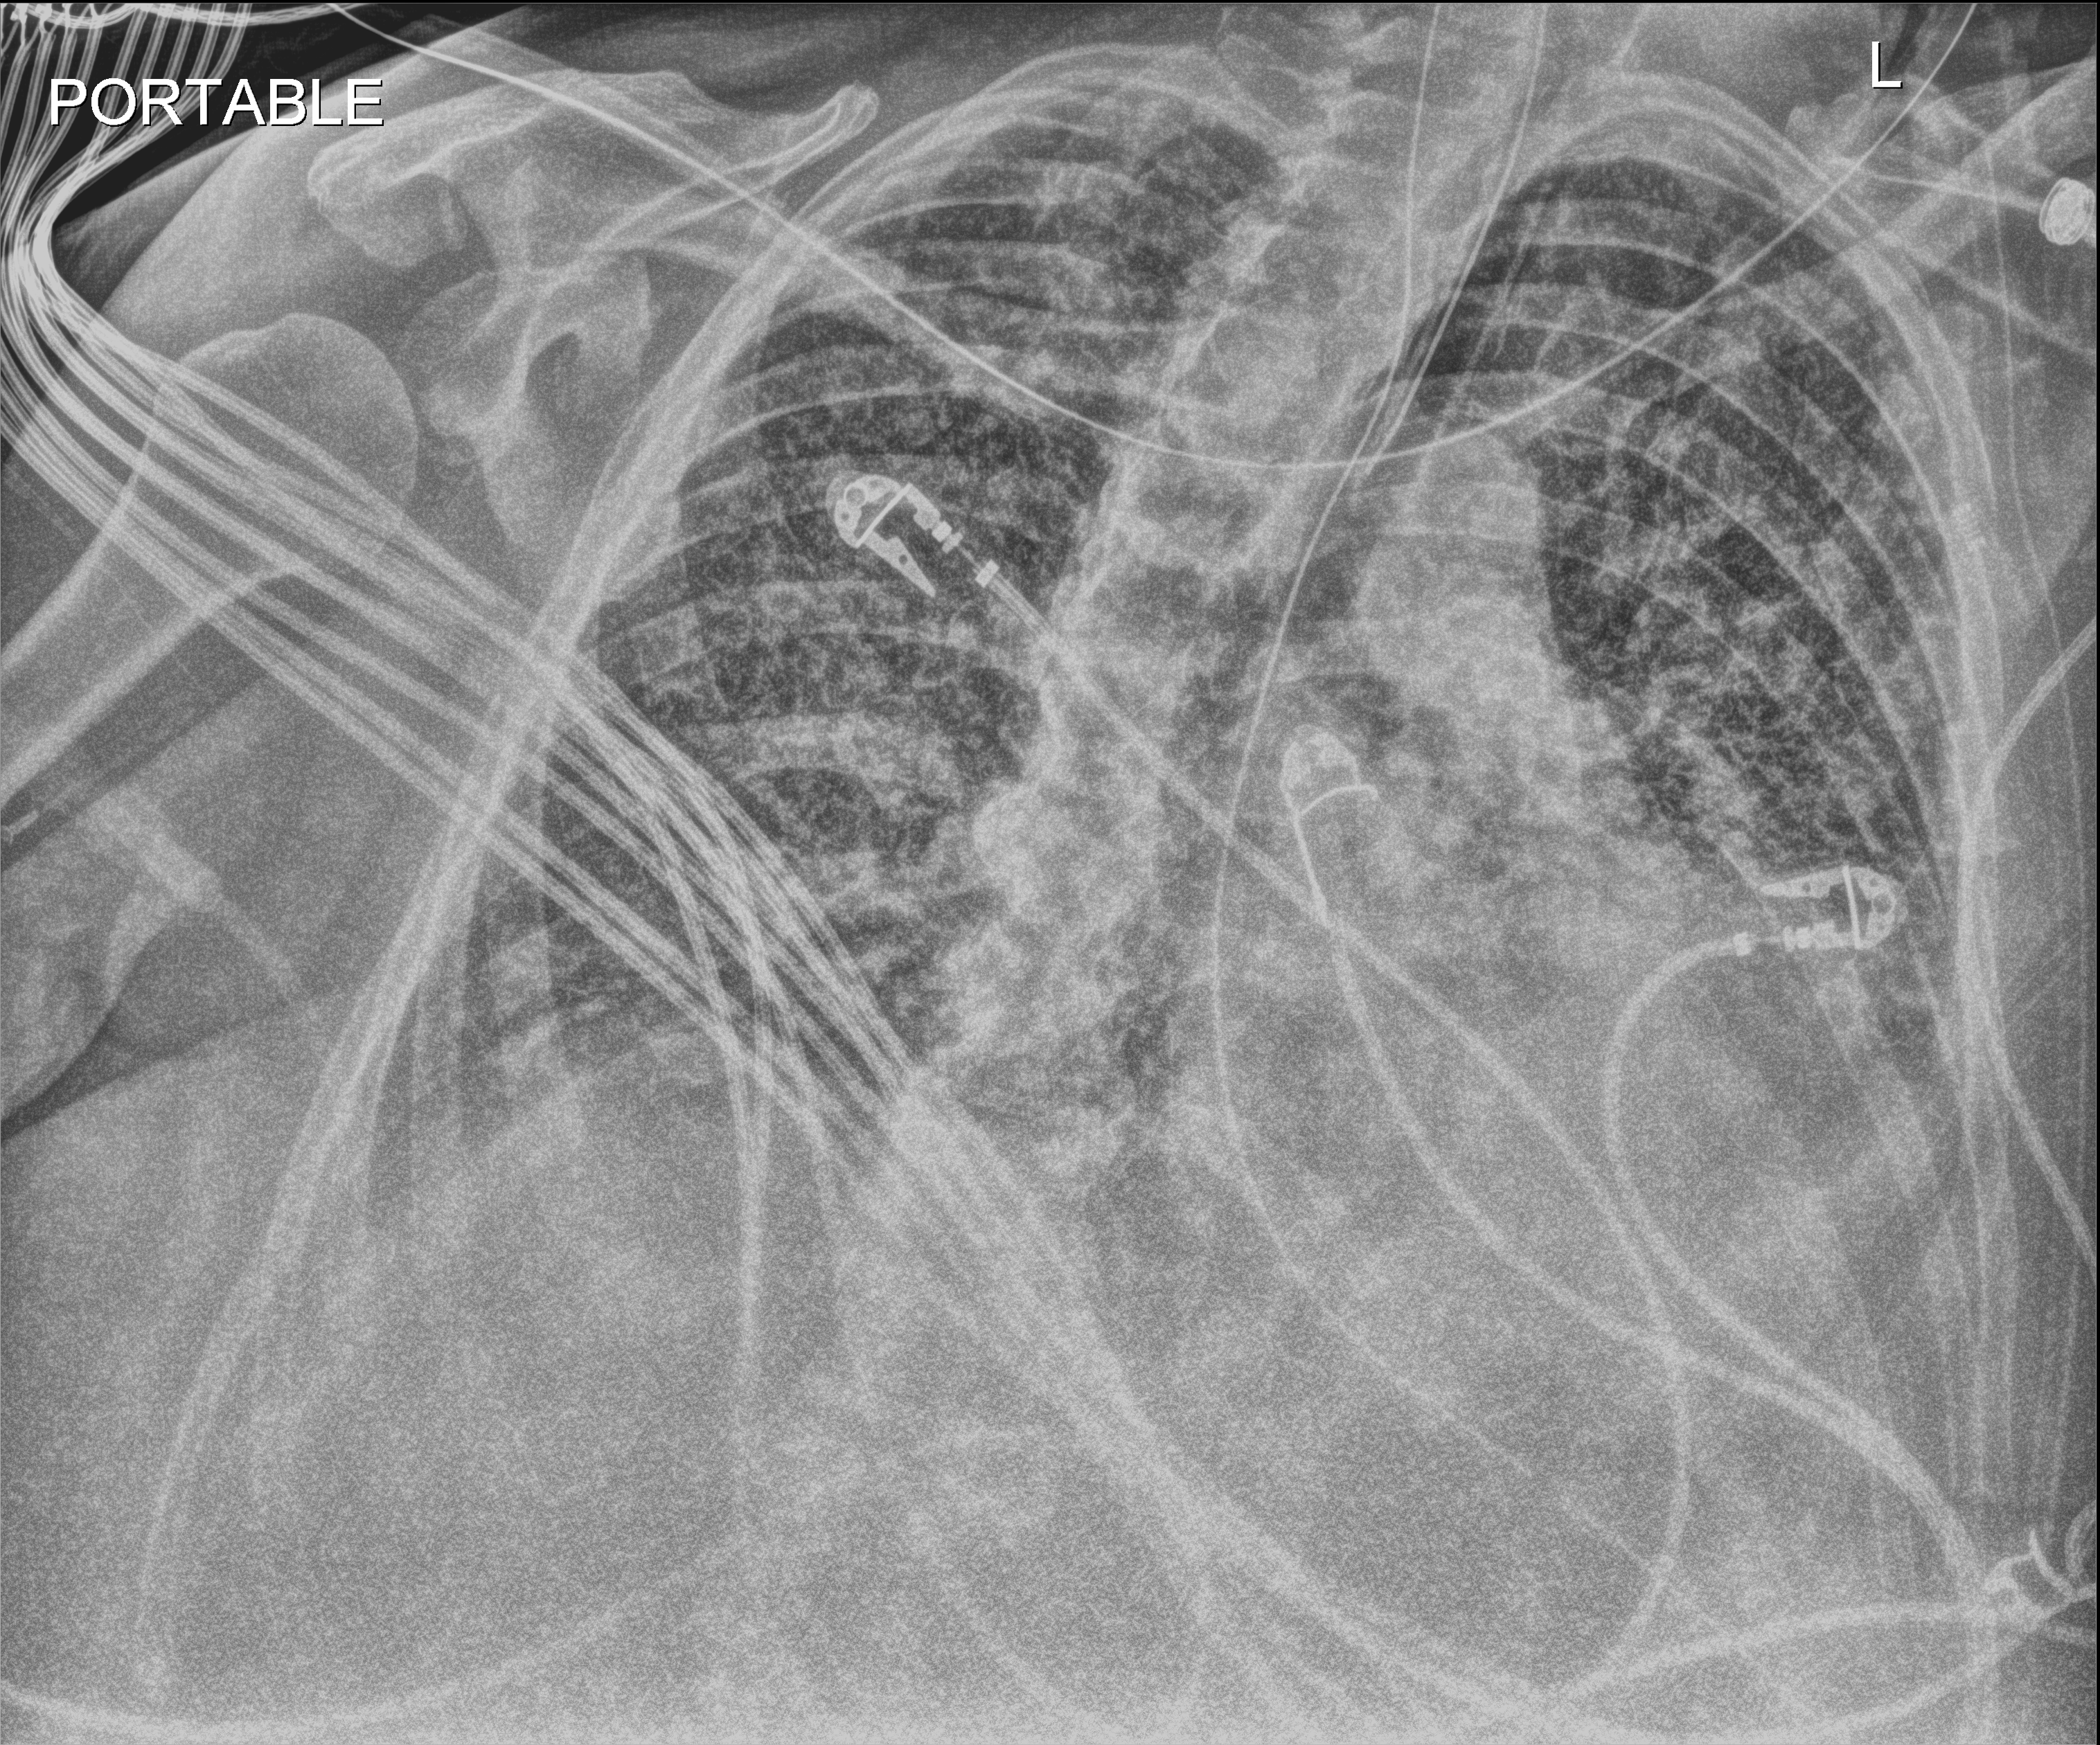
Portable chest radiograph; anteroposterior (AP) projection. Adult patient hospitalised with COVID-19, age 18–59 years.
Hospital-stay facts (about this admission, not read from this image; timing relative to this image not recorded):
- length of hospital stay: 28 days
- mechanically ventilated during this hospital stay: yes